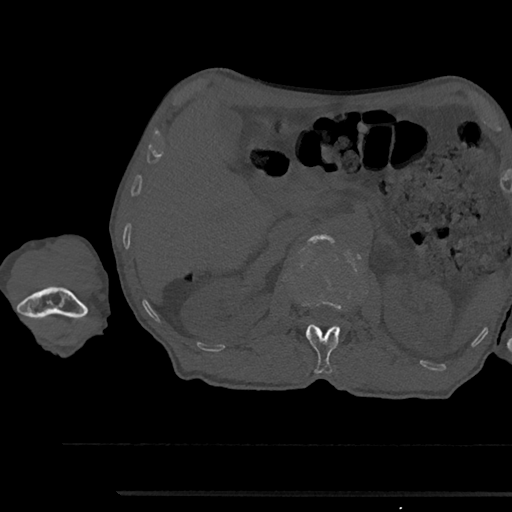
CT including the spine, one axial slice. Position 616 of 797 along the scan axis. Reconstruction kernel Br40s/3. Bone window (W 1800 / L 400 HU). 0.5 mm slice thickness. 512 × 512 image matrix. Patient: male, 79 years. From the clinical record (not read from this slice): primary cancer: prostate.
Outlined on this slice (semi-automatic segmentation, software-assisted and operator-edited):
- L1 vertebra: bounding box [x1, y1, x2, y2] px = [295, 295, 341, 374]
- L2 vertebra: [308, 234, 335, 305]